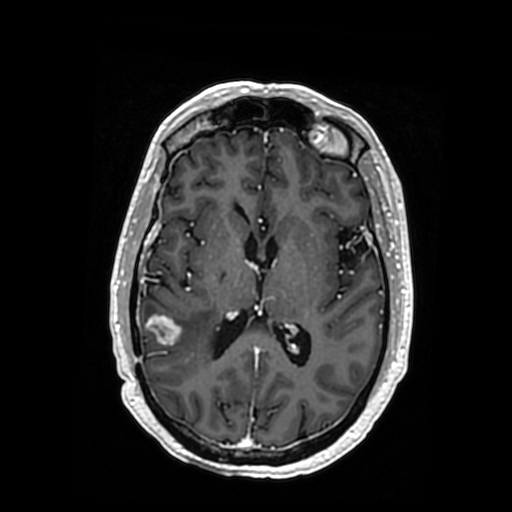
Brain MRI from a brain-tumour surgery series, one axial slice; position 173 of 364 along the scan axis; T1-weighted post-contrast; 0.5 mm slice thickness; 512 × 512 image matrix. From the clinical record (not read from this slice): histopathology: Oligodendroglioma; WHO grade: 3; IDH mutation: yes; tumour location: Right Posterior Temporal Inferior Parietal.
Outlined on this slice (outlined manually by an expert reader):
- tumour: bounding box [x1, y1, x2, y2] px = [148, 315, 182, 372]